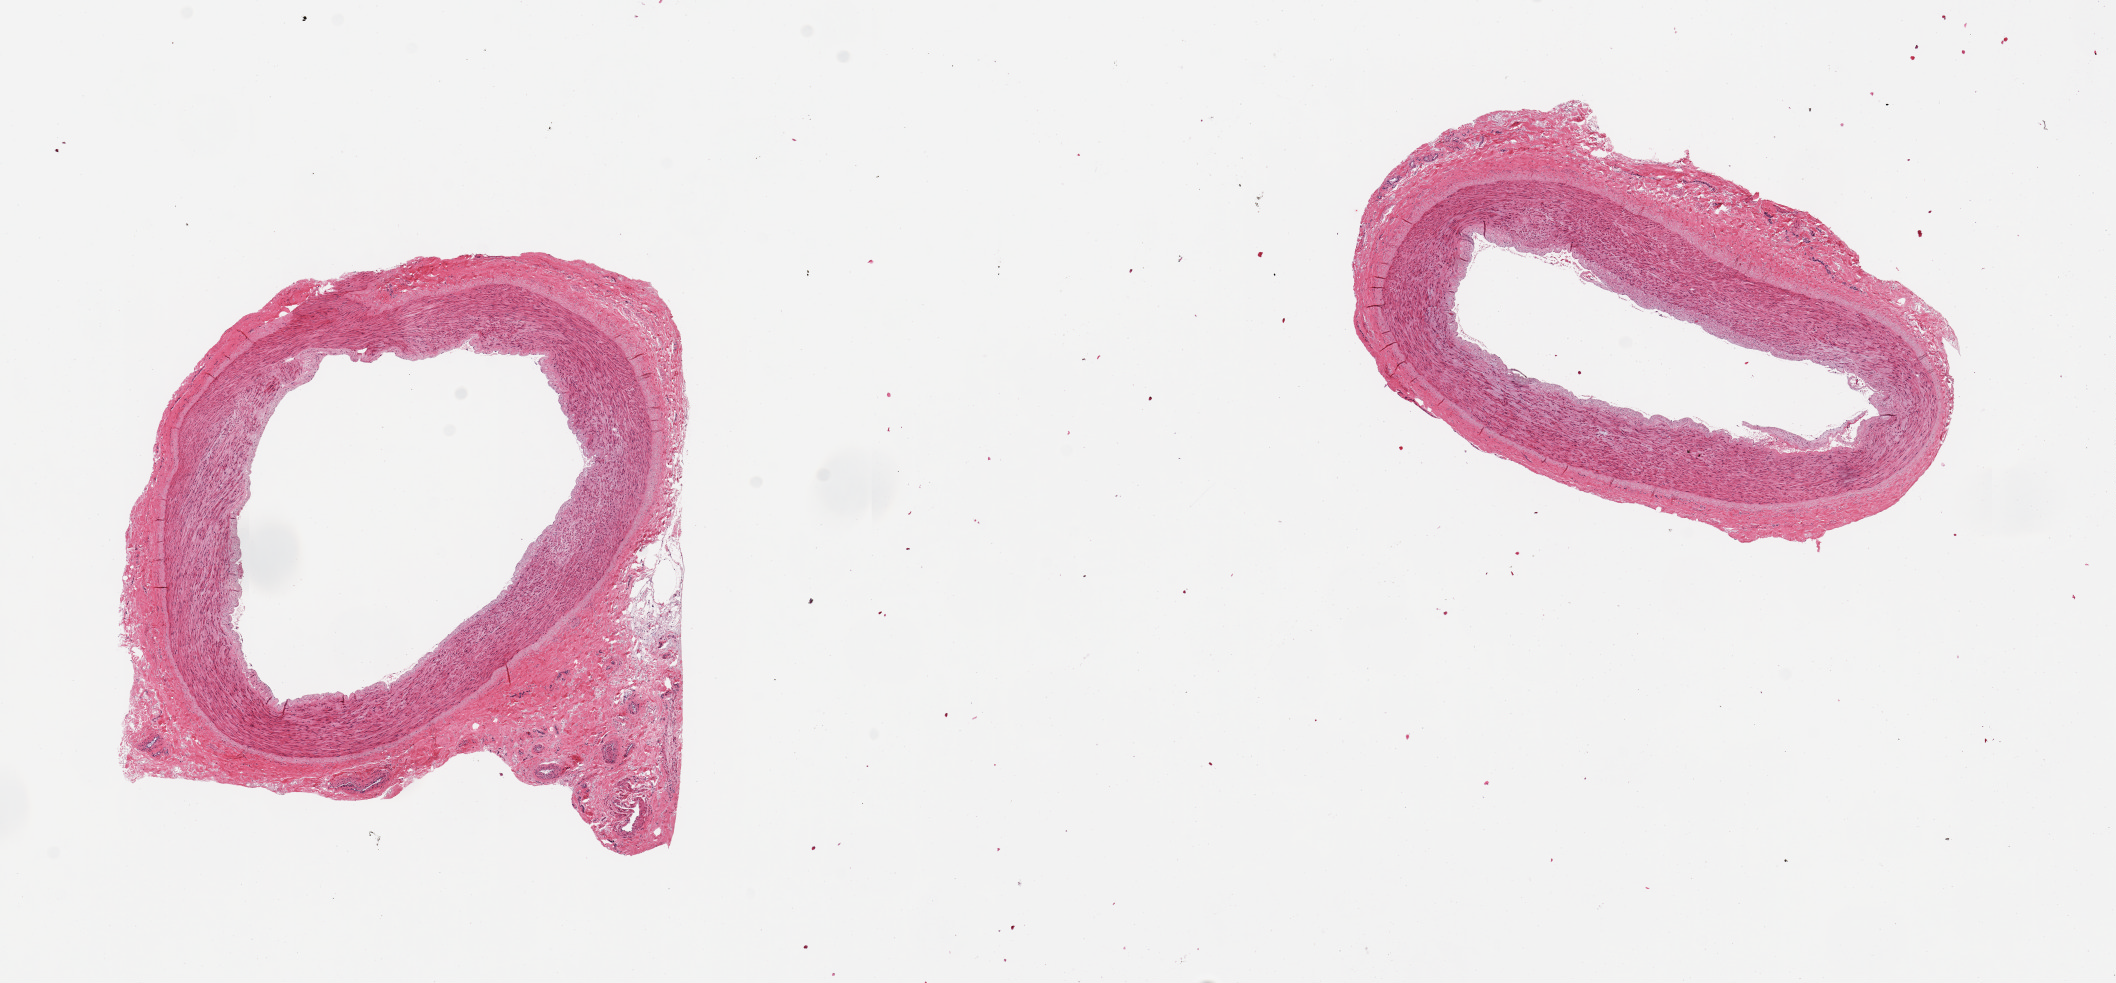
H&E whole-slide image — whole scanned area (about 16.7 x 7.8 mm) shown as a low-resolution overview; PAXgene-fixed paraffin-embedded (PFPE) section; sampled site (target tissue): tibial artery; donor tissue sample. Donor: female.
Reviewer comment on this tissue sample: 2 pieces.